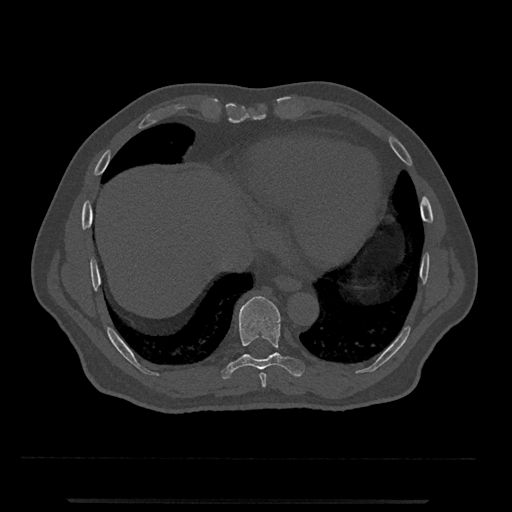
CT including the spine, one axial slice. Position 575 of 797 along the scan axis. Reconstruction kernel Br40s/3. Bone window (W 1800 / L 400 HU). 512 × 512 image matrix. Male patient, age 63 years. From the clinical record (not read from this slice): primary cancer: prostate.
Structures marked on this image (semi-automatic segmentation, software-assisted and operator-edited):
- T8 vertebra: bounding box (x1, y1, x2, y2) in pixels: (259, 372, 267, 388)
- T9 vertebra: (221, 296, 305, 379)